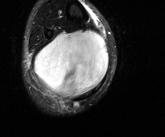
MRI of an extremity soft-tissue mass, one axial slice; position 46 of 81 along the scan axis; T2-weighted fat-saturated; MR volume resampled by the dataset authors to the PET/CT grid (not the native acquisition matrix); 3.27 mm slice thickness; 165 × 137 image matrix, field of view 161 × 134 mm. Male patient. Case-level facts recorded for this patient, not image findings: histological type: liposarcoma - round cell; grade: high; site of the primary tumour: right calf.
Structures marked on this image (expert contour drawn on MRI and transferred to this co-registered scan by the dataset authors):
- gross tumour volume (mass): bounding box <34,30,109,99> (left, top, right, bottom; pixels)